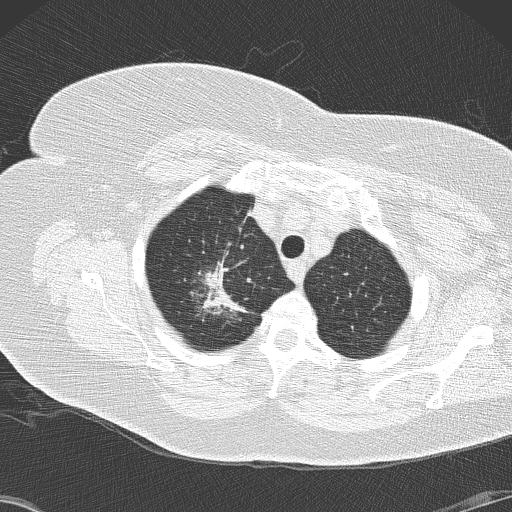
Low-dose screening chest CT, axial slice; second screening round (one year after baseline); lung window (W 1500 / L -600 HU); lung (sharp) reconstruction kernel (B50f); slice 24 of 146 in the series. Female participant, aged 72 years at enrolment.
- Expert reader's lesion annotation, box from (x=181, y=244) to (x=260, y=327) px.
- The screening reader recorded 4 non-calcified nodules or masses ≥4 mm on this exam (right lower lobe, right lower lobe, right lower lobe, right upper lobe); which of them this box marks is not recorded.
- Lung cancer was diagnosed 52 days after this screen: bronchiolo-alveolar adenocarcinoma, NOS, right upper lobe, stage IIIB (AJCC 6th edition), 45 mm at pathology.